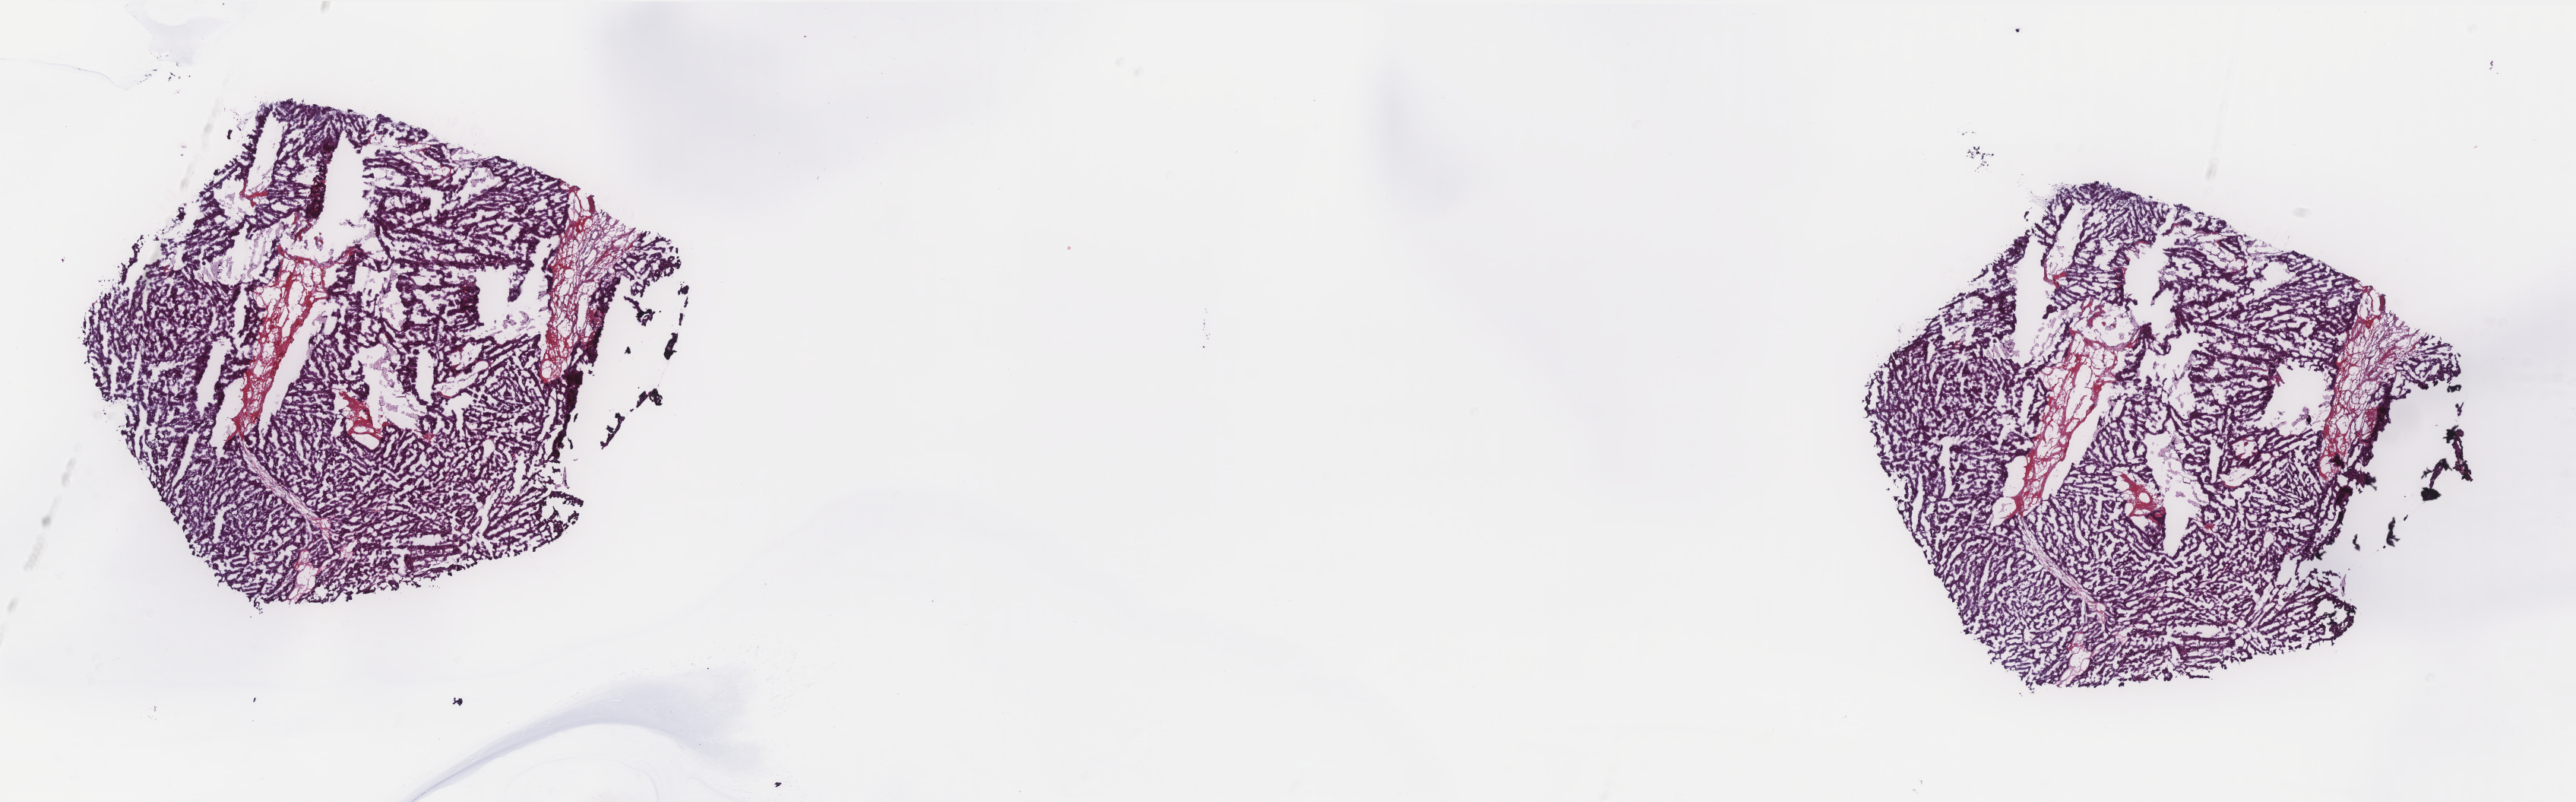
H&E whole-slide image — whole scanned area (about 27.2 x 8.5 mm, acquisition: 40x scan) shown as a low-resolution overview. Frozen section from the top of the tissue portion. Sample: primary tumour, liver. Male, age 68 years at initial diagnosis. Histologic grade: G2 (moderately differentiated). Composition of this section per pathologist review: tumour cells 100%, tumour nuclei 90%, normal cells 0%, stromal cells 0%, necrosis 0%. Inflammatory infiltration, as recorded: lymphocyte infiltration 0%, monocyte infiltration 0%, neutrophil infiltration 0%.
Histologic diagnosis: Hepatocellular carcinoma, NOS. TNM: T2 N0 M0. AJCC pathologic stage: II (5th edition).